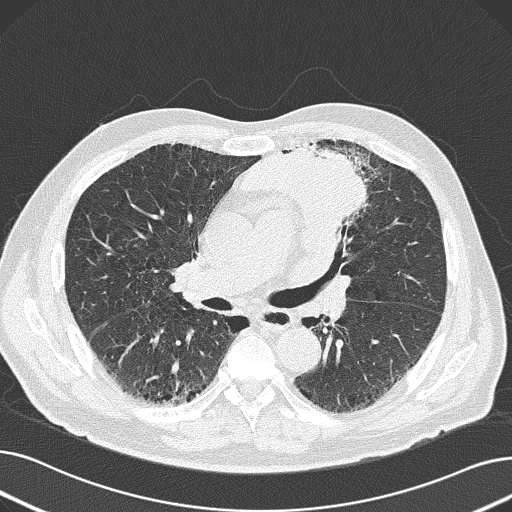
Chest CT (low-dose screening protocol), one axial image; baseline screening round; lung window (W 1500 / L -600 HU); 2 mm slice thickness; lung (sharp) reconstruction kernel (B50f); slice 79 of 165 in the series; 512 × 512 image matrix, field of view 370 × 370 mm. Male participant, aged 69 years at enrolment. Former smoker at enrolment.
Expert-annotated lung lesion, bounding box (x1, y1, x2, y2) in pixels: (238, 130, 386, 249). Screening reader's record for this exam (one nodule recorded; not confirmed to be the boxed lesion): non-calcified nodule or mass ≥4 mm, left upper lobe, 6 × 10 mm, spiculated (stellate) margins, soft tissue attenuation. Official screen result: positive, change unspecified: nodule(s) >= 4 mm or enlarging nodule(s), mass(es), or other non-specific abnormalities suspicious for lung cancer.